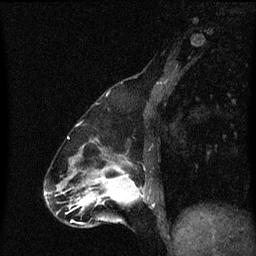
Breast MRI (dynamic contrast-enhanced), one sagittal slice. Slice 24 of 60 in the series (ordered by position). Dynamic contrast-enhanced series, image 2 of 3 at this slice position (ordered by acquisition). 1.5 T. TE 4.2 ms, TR 8.4 ms. 256 × 256 image matrix, field of view 200 × 200 mm. Female patient, age 47 years.
Outlined on this slice (semi-automatically segmented with operator editing):
- analysis volume of interest (the breast-tissue region the enhancement analysis was run in; not a lesion): bounding box [x1, y1, x2, y2] px = [100, 172, 151, 219]
- tumour enhancement mask (voxels above the 70 % enhancement threshold inside the analysis volume of interest): [100, 172, 145, 205]